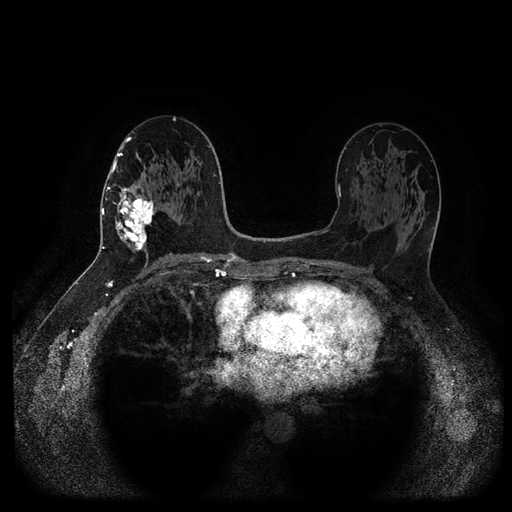
Breast MRI (dynamic contrast-enhanced, multi-phase), one axial slice; position 55 of 116 along the scan axis; dynamic contrast-enhanced series, time point 2 of 5 at this slice position (early post-contrast); 1.5 T; TE 2.6 ms, TR 5.3 ms; 512 × 512 image matrix, field of view 360 × 360 mm. Patient: female, 58 years.
Structures marked on this image (semi-automatically segmented with operator editing):
- breast lesion (labelled 'tumour' in the annotation; benign lesions carry a separate 'benign' label): box from (x=112, y=186) to (x=158, y=254) px